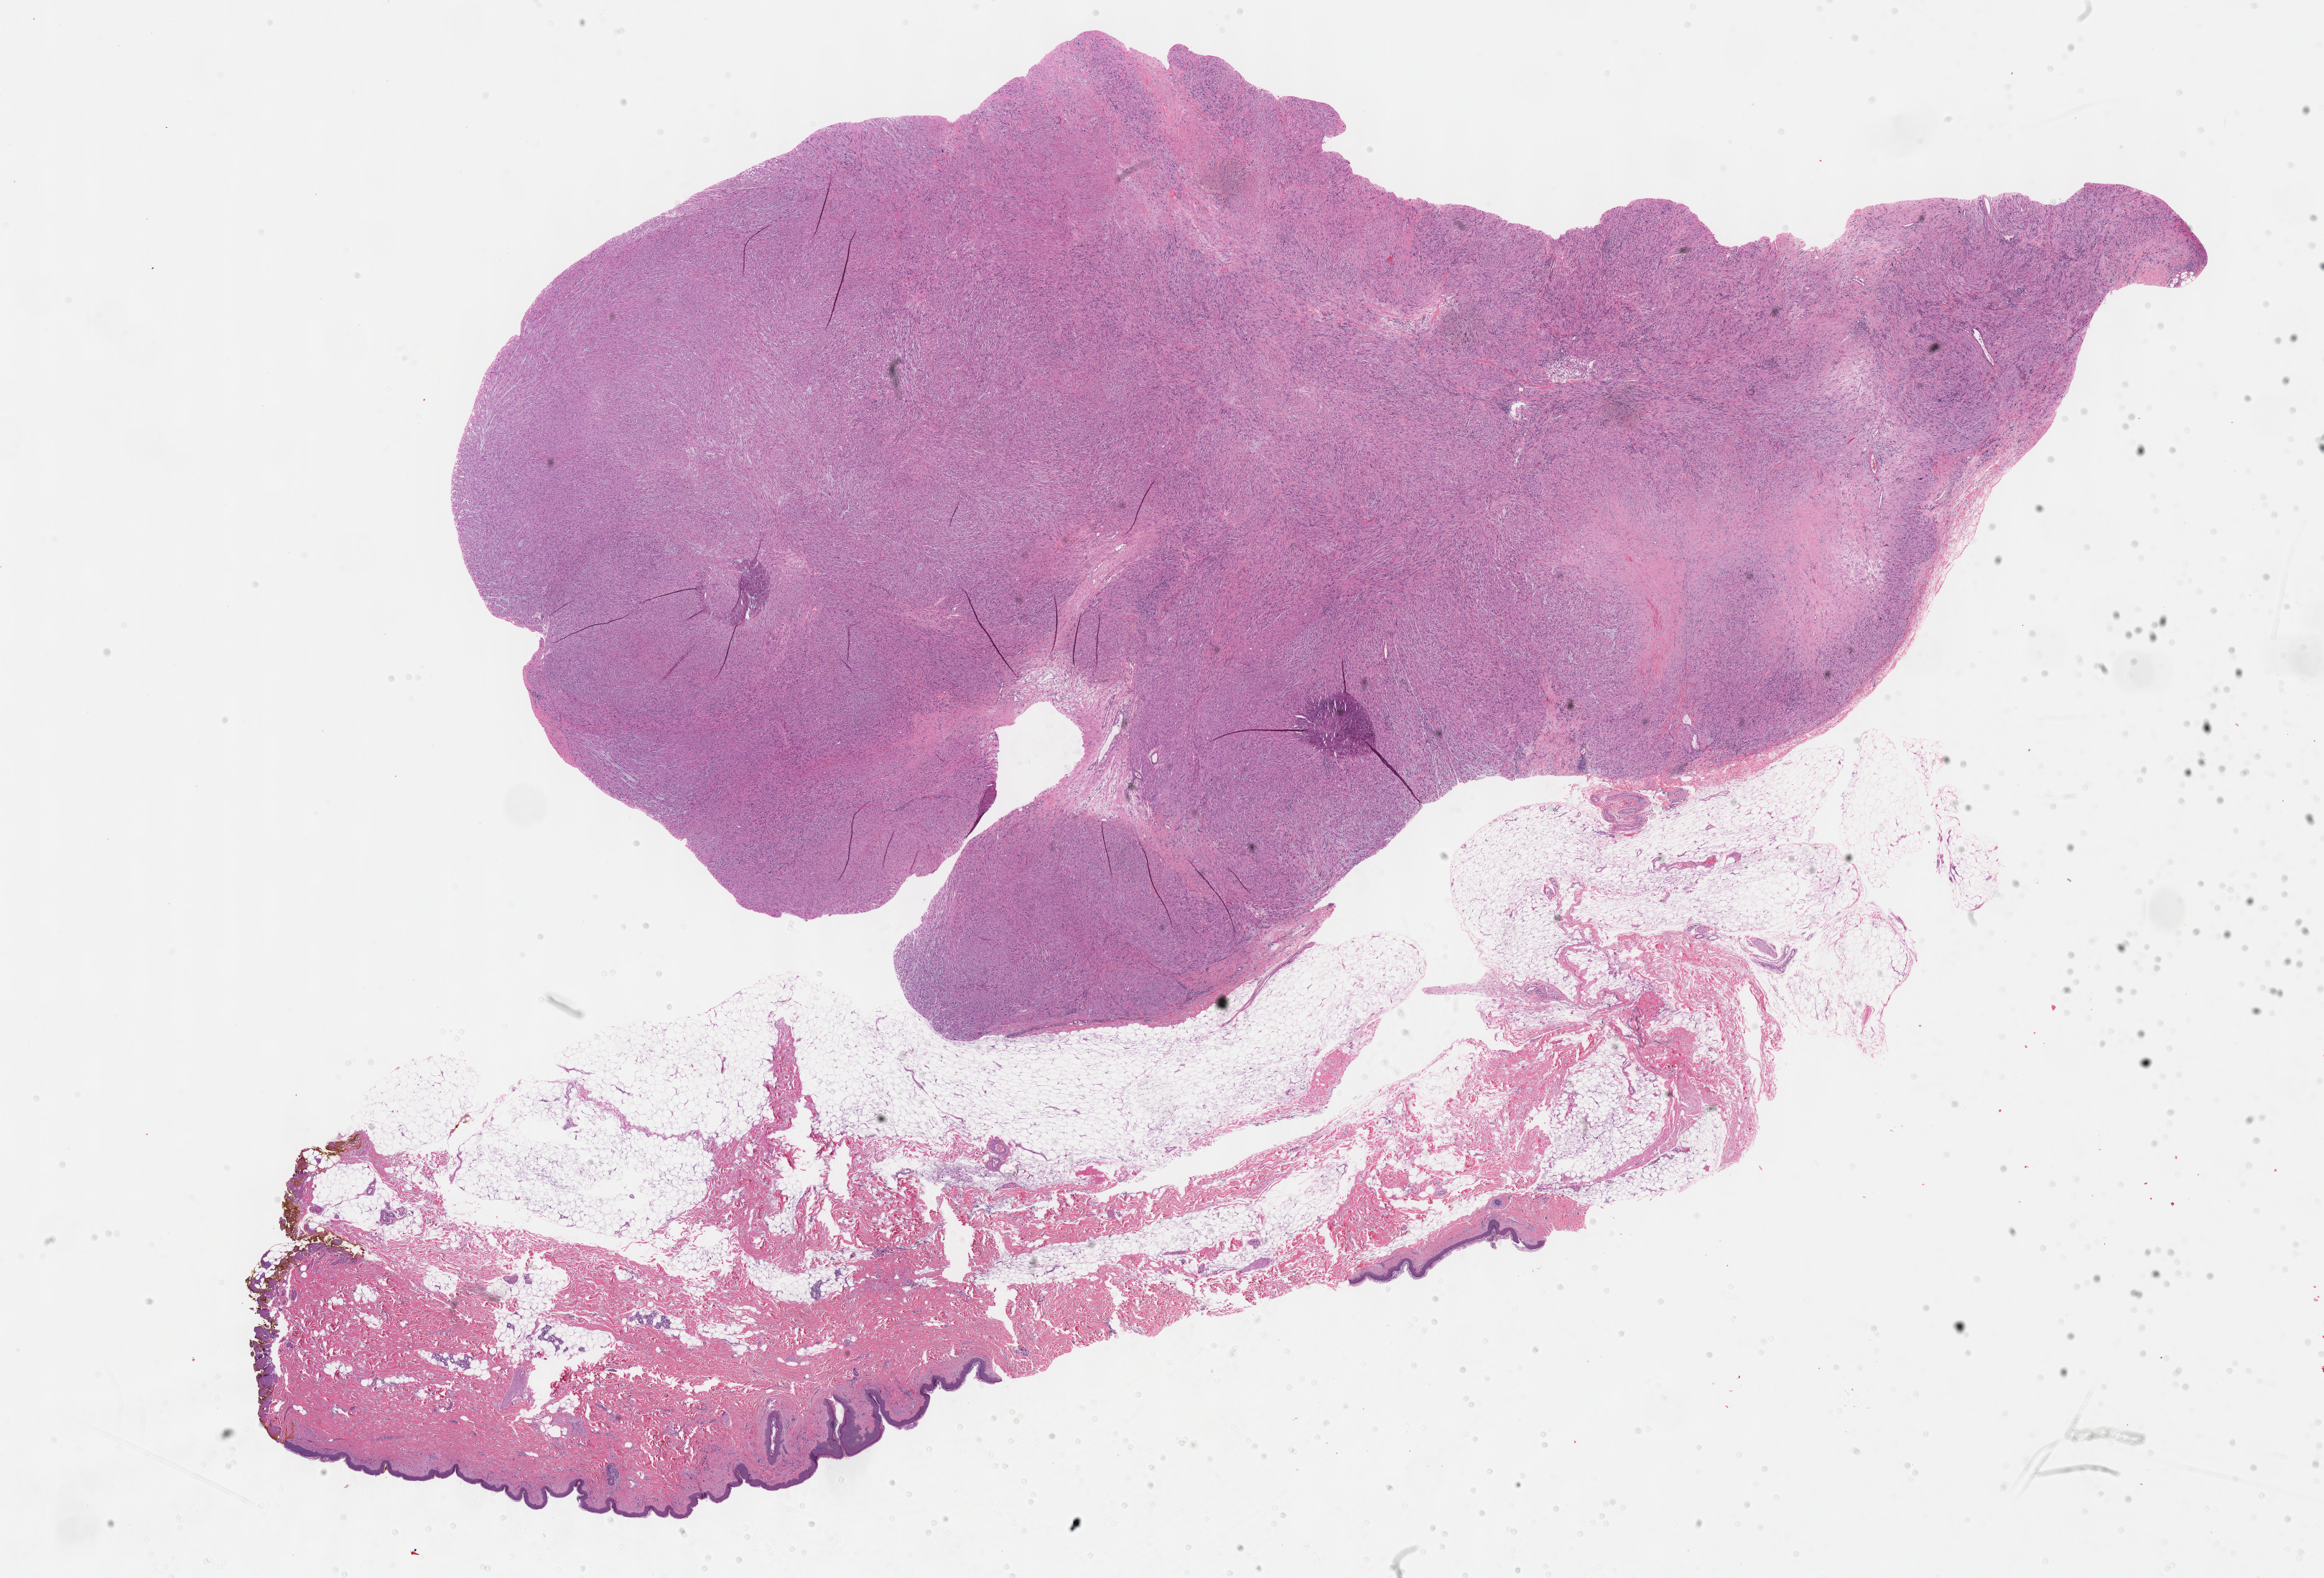
Digitized H&E tissue section (whole slide) — whole scanned area (about 26.2 x 17.8 mm) shown as a low-resolution overview. Formalin-fixed paraffin-embedded (FFPE) diagnostic section. Connective, subcutaneous and other soft tissues, primary tumour sample. Female, age 82 years at initial diagnosis.
Diagnosis: Leiomyosarcoma, NOS (connective, subcutaneous and other soft tissues of lower limb and hip).